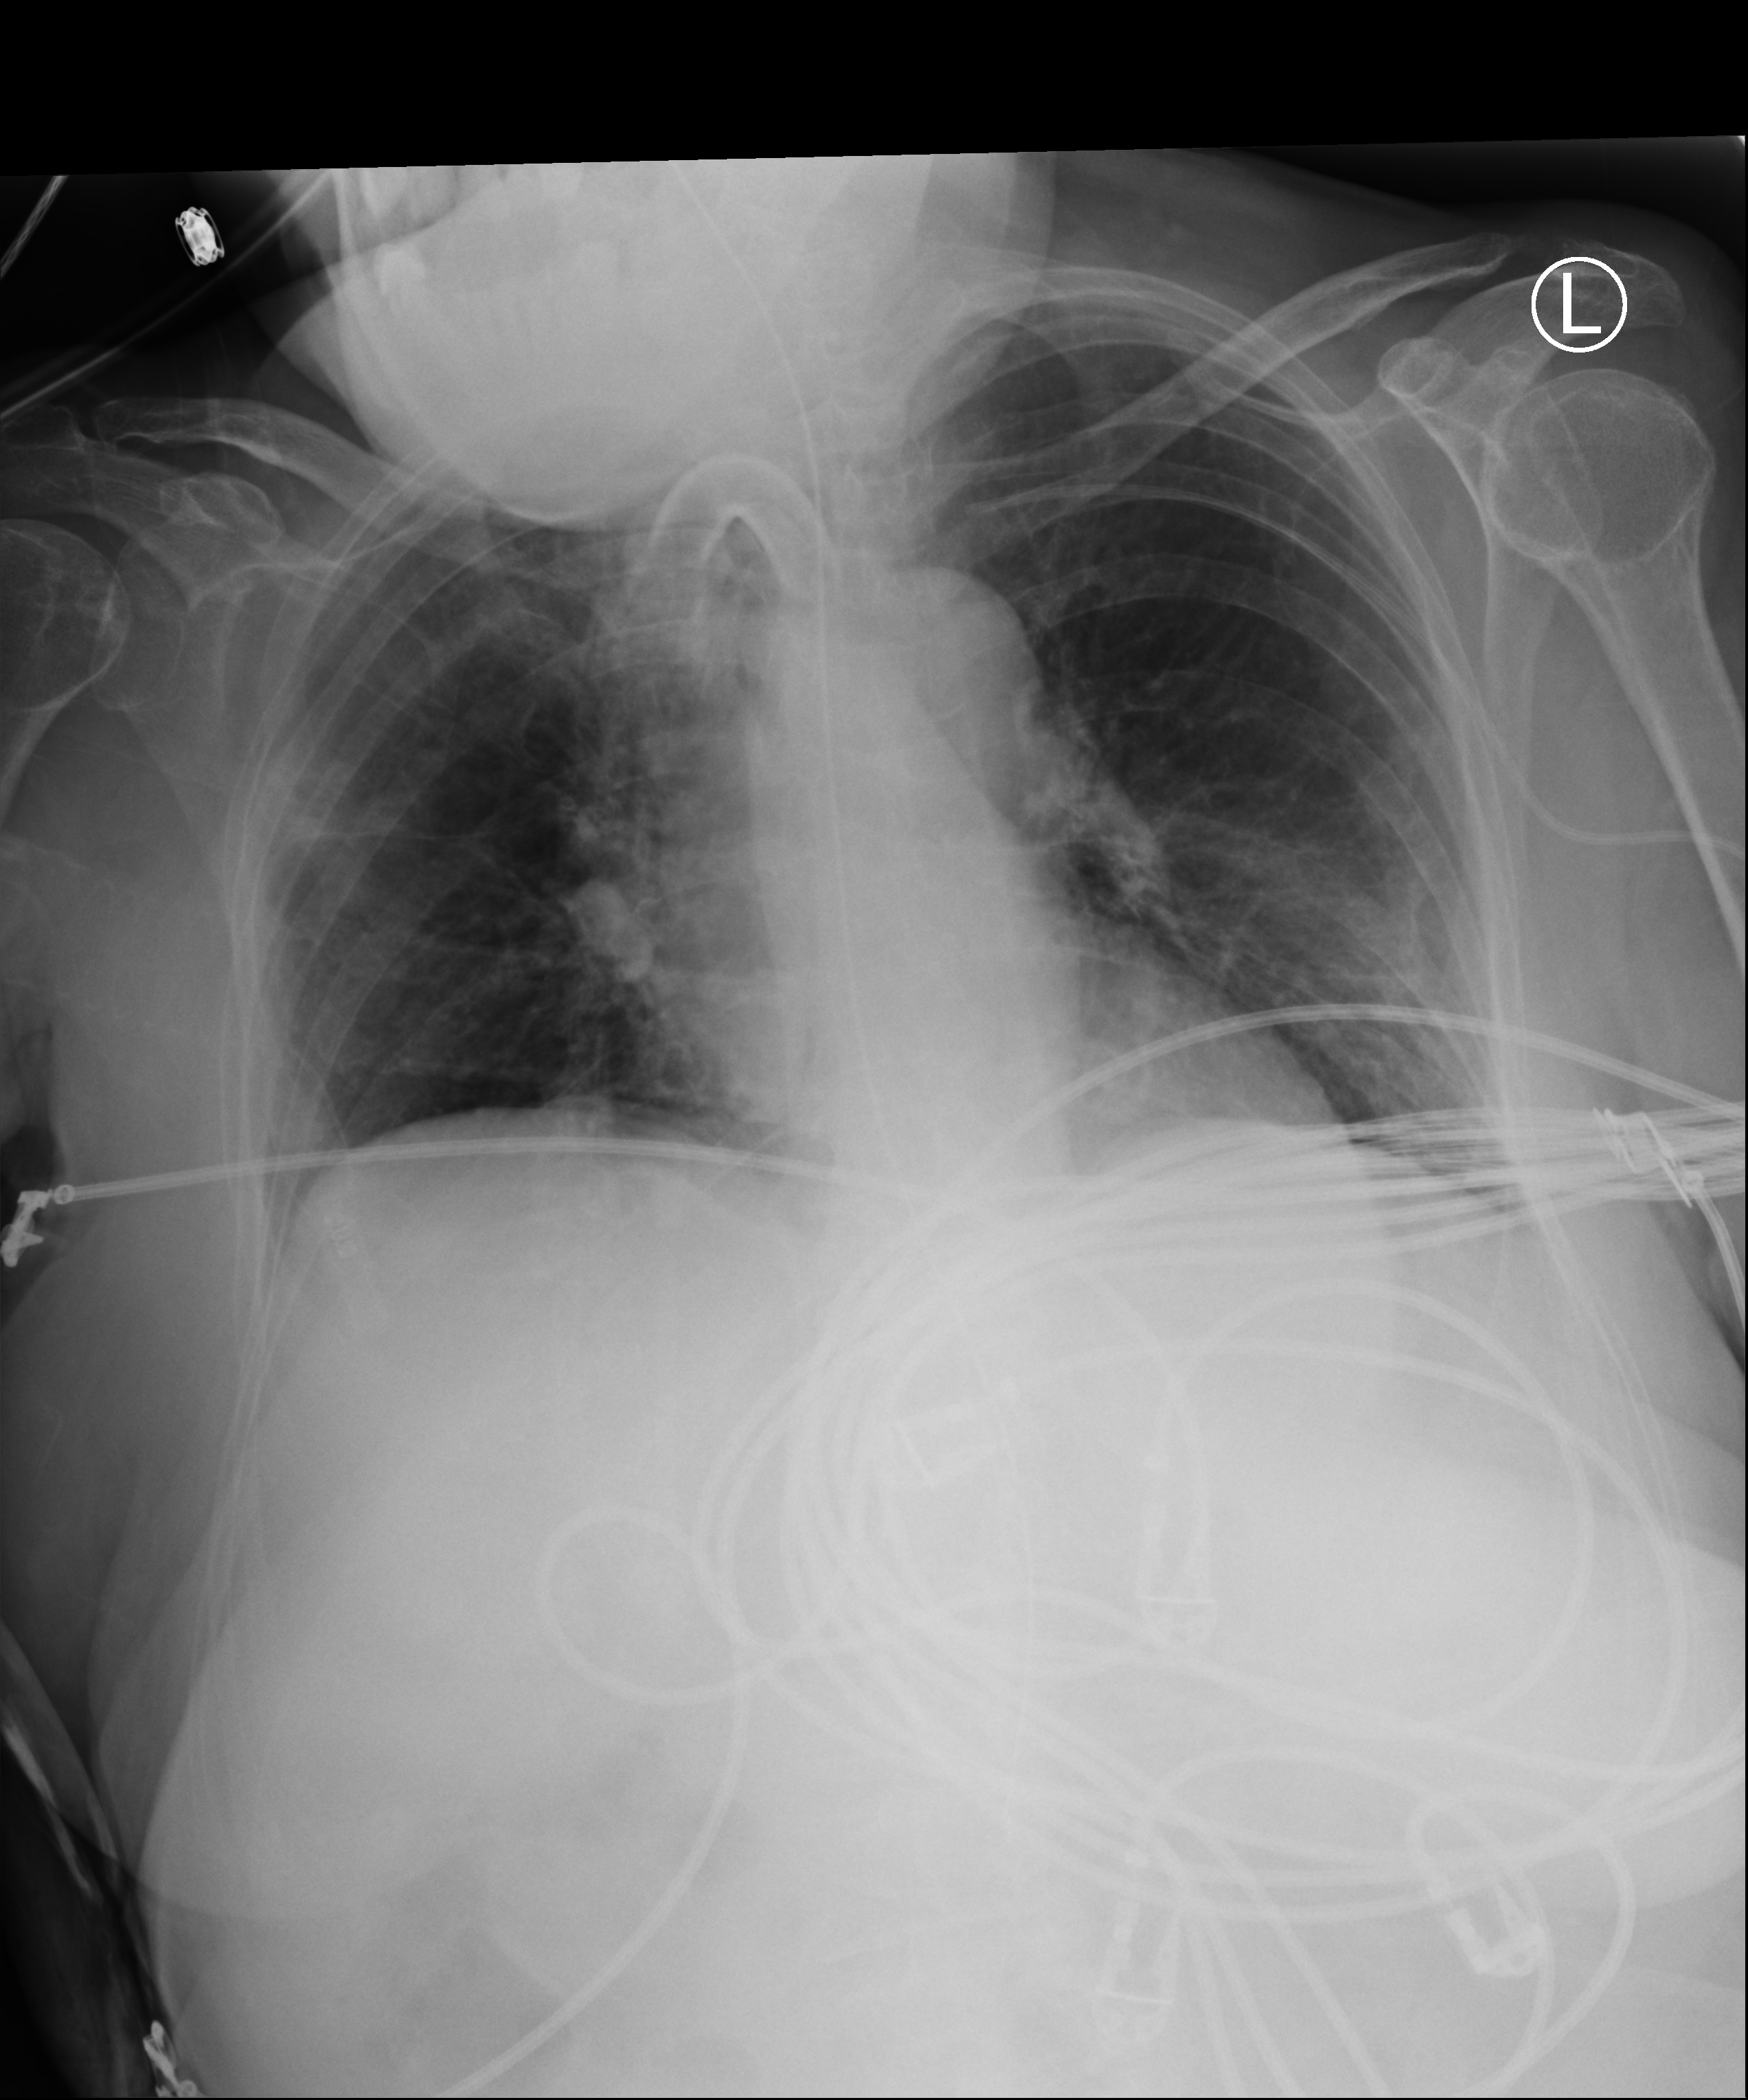
Bedside chest radiograph (computed radiography); anteroposterior (AP) projection. Patient hospitalised with COVID-19; female, aged 75–90 years.
Admission-level facts for this patient (not findings on this image; timing relative to this image not recorded):
- mechanically ventilated during this hospital stay: yes